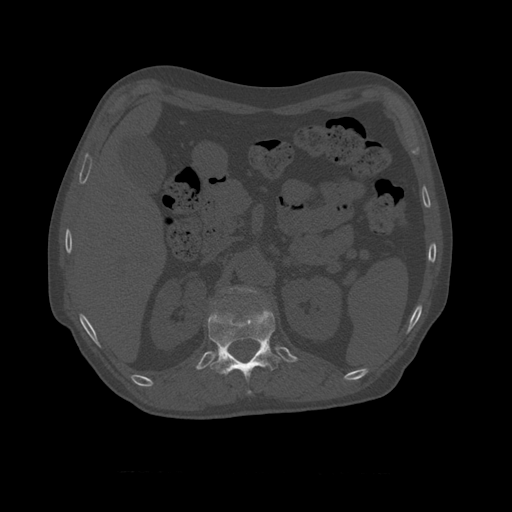
CT including the spine, one axial slice. Slice 376 of 450 in the series (ordered by position). Reconstruction kernel STANDARD. Bone window (W 1800 / L 400 HU). 1.25 mm slice thickness. 512 × 512 image matrix. Patient age 75 years. Case-level facts recorded for this patient, not image findings: primary cancer: prostate.
Structures marked on this image (semi-automatically segmented with operator editing):
- L1 vertebra: bounding box <221,287,258,296> (left, top, right, bottom; pixels)
- T11 vertebra: <208,305,281,395>